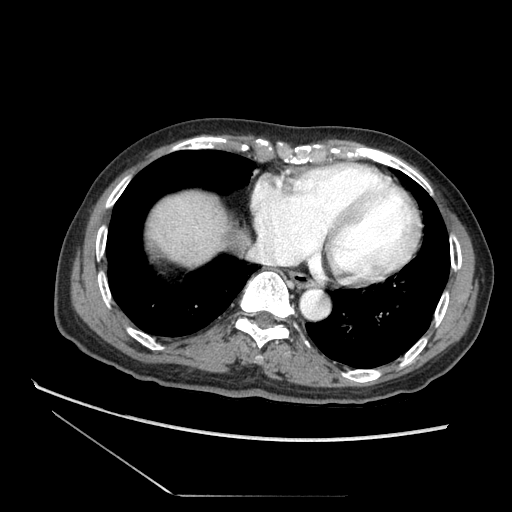
Contrast-enhanced abdominal CT (liver protocol), one axial slice. Slice 72 of 73 in the series (ordered by position). 120 kVp. Soft-tissue window (W 400 / L 40 HU). 512 × 512 image matrix. Case-level facts recorded for this patient, not image findings: diagnosis: hepatocellular carcinoma (patient treated with transarterial chemoembolisation; whether this scan precedes or follows treatment is not stated here); TNM stage (as recorded): Stage-II; Child-Pugh class: A; tumour differentiation: moderately differentiated; tumour nodularity: multinodular.
Structures marked on this image (semi-automatic segmentation, software-assisted and operator-edited):
- abdominal aorta: bounding box [x1, y1, x2, y2] px = [302, 290, 331, 319]
- liver parenchyma outside the tumour (the mass and vessels are separate outlines, so this box may not span the whole liver): [138, 182, 242, 283]